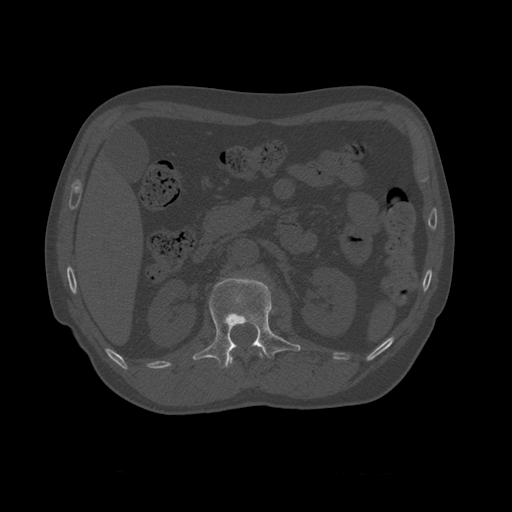
CT including the spine, one axial slice; position 356 of 450 along the scan axis; reconstruction kernel STANDARD; 120 kVp; bone window (W 1800 / L 400 HU); 1.25 mm slice thickness; 512 × 512 image matrix, field of view 405 × 405 mm. Patient age 75 years. From the clinical record (not read from this slice): primary cancer: prostate.
Outlined on this slice (semi-automatic segmentation, software-assisted and operator-edited):
- L1 vertebra: bounding box <193,274,302,369> (left, top, right, bottom; pixels)
- T10 vertebra: <224,345,264,367>
- T11 vertebra: <226,353,263,368>